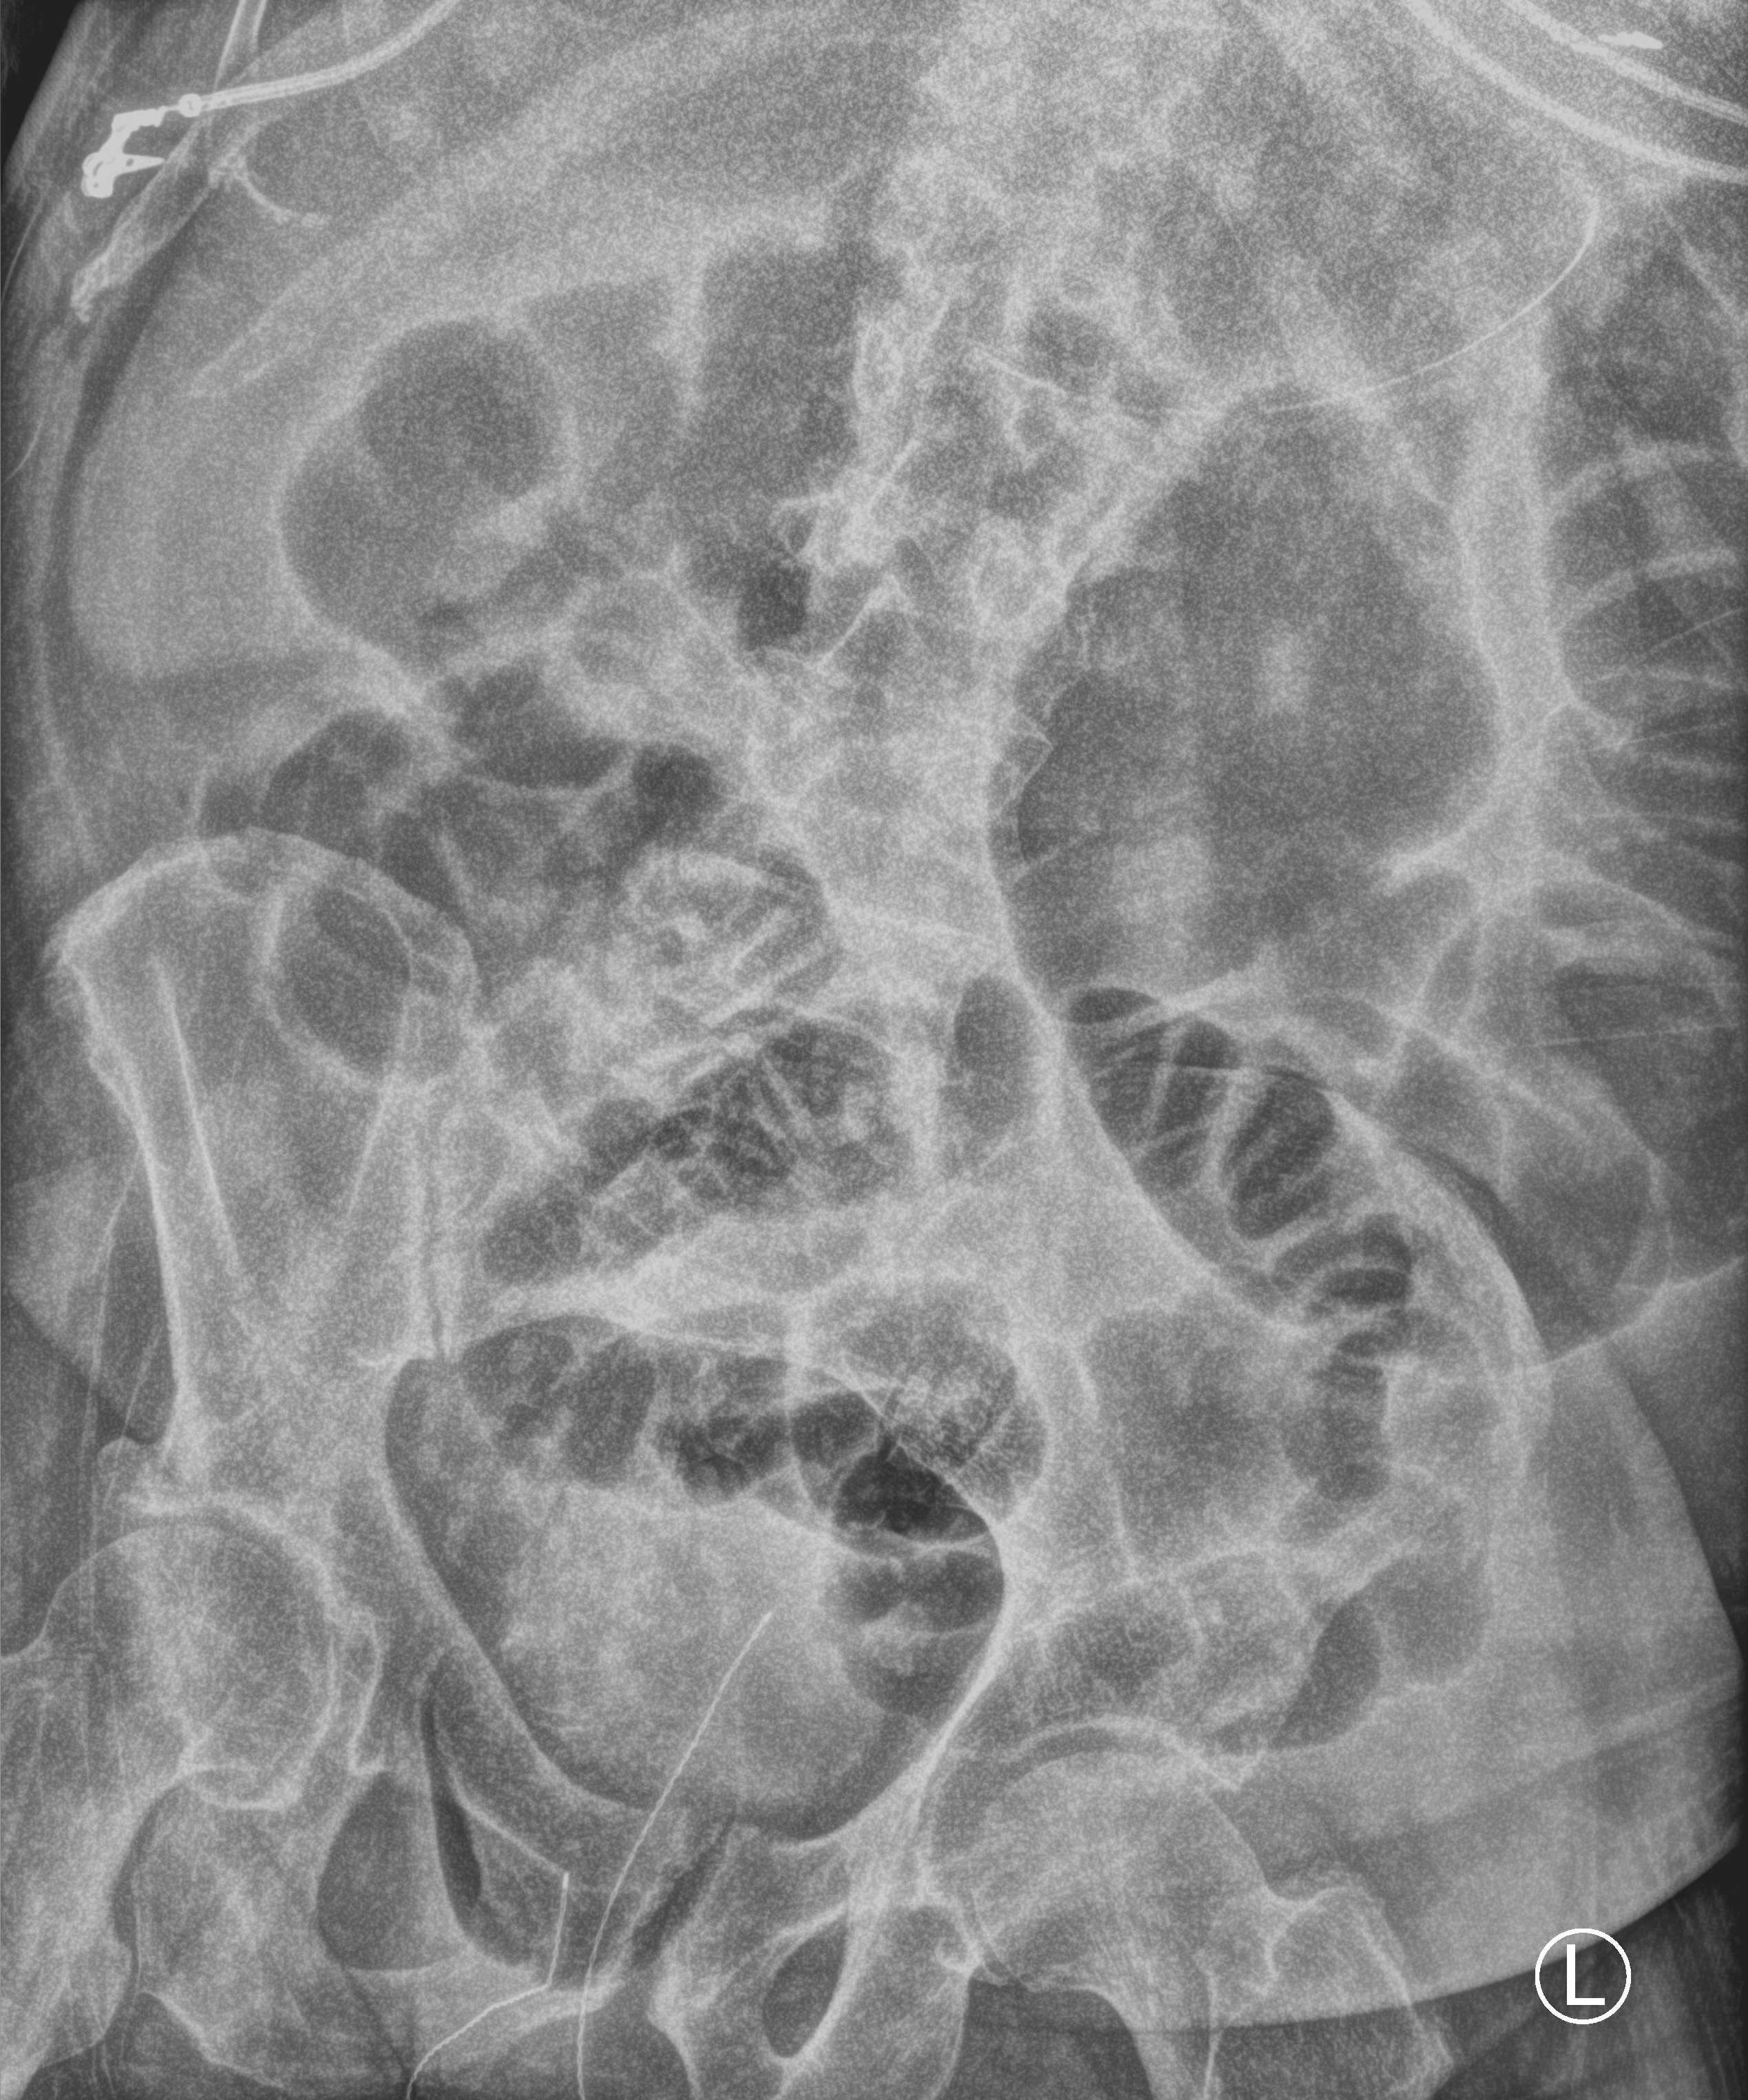
Portable abdomen radiograph; anteroposterior (AP) projection. Patient hospitalised with COVID-19; male, aged 60–74 years.
Admission-level facts for this patient (not findings on this image; timing relative to this image not recorded): smoking status (admission record): never.